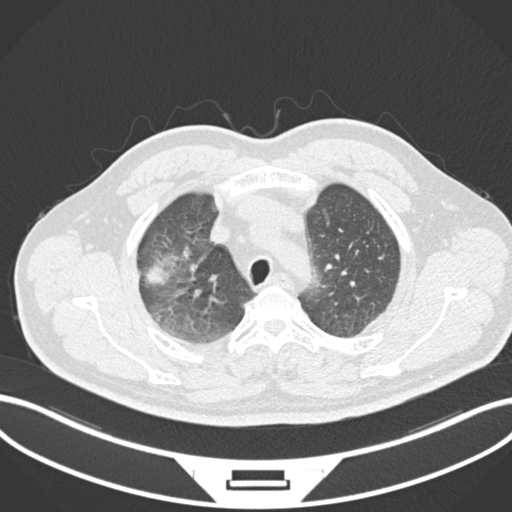
Chest CT, one axial slice; position 684 of 852 along the scan axis; 120 kVp; lung window (W 1500 / L -600 HU); 512 × 512 image matrix, field of view 400 × 400 mm. Male patient, age 55 years. Case-level facts recorded for this patient, not image findings: clinical TNM (as recorded): T3 N2 M1.
Annotated regions visible in this slice (bounding box drawn by a radiologist):
- lung tumour (recorded histology: adenocarcinoma): bounding box (x1, y1, x2, y2) in pixels: (147, 245, 183, 290)